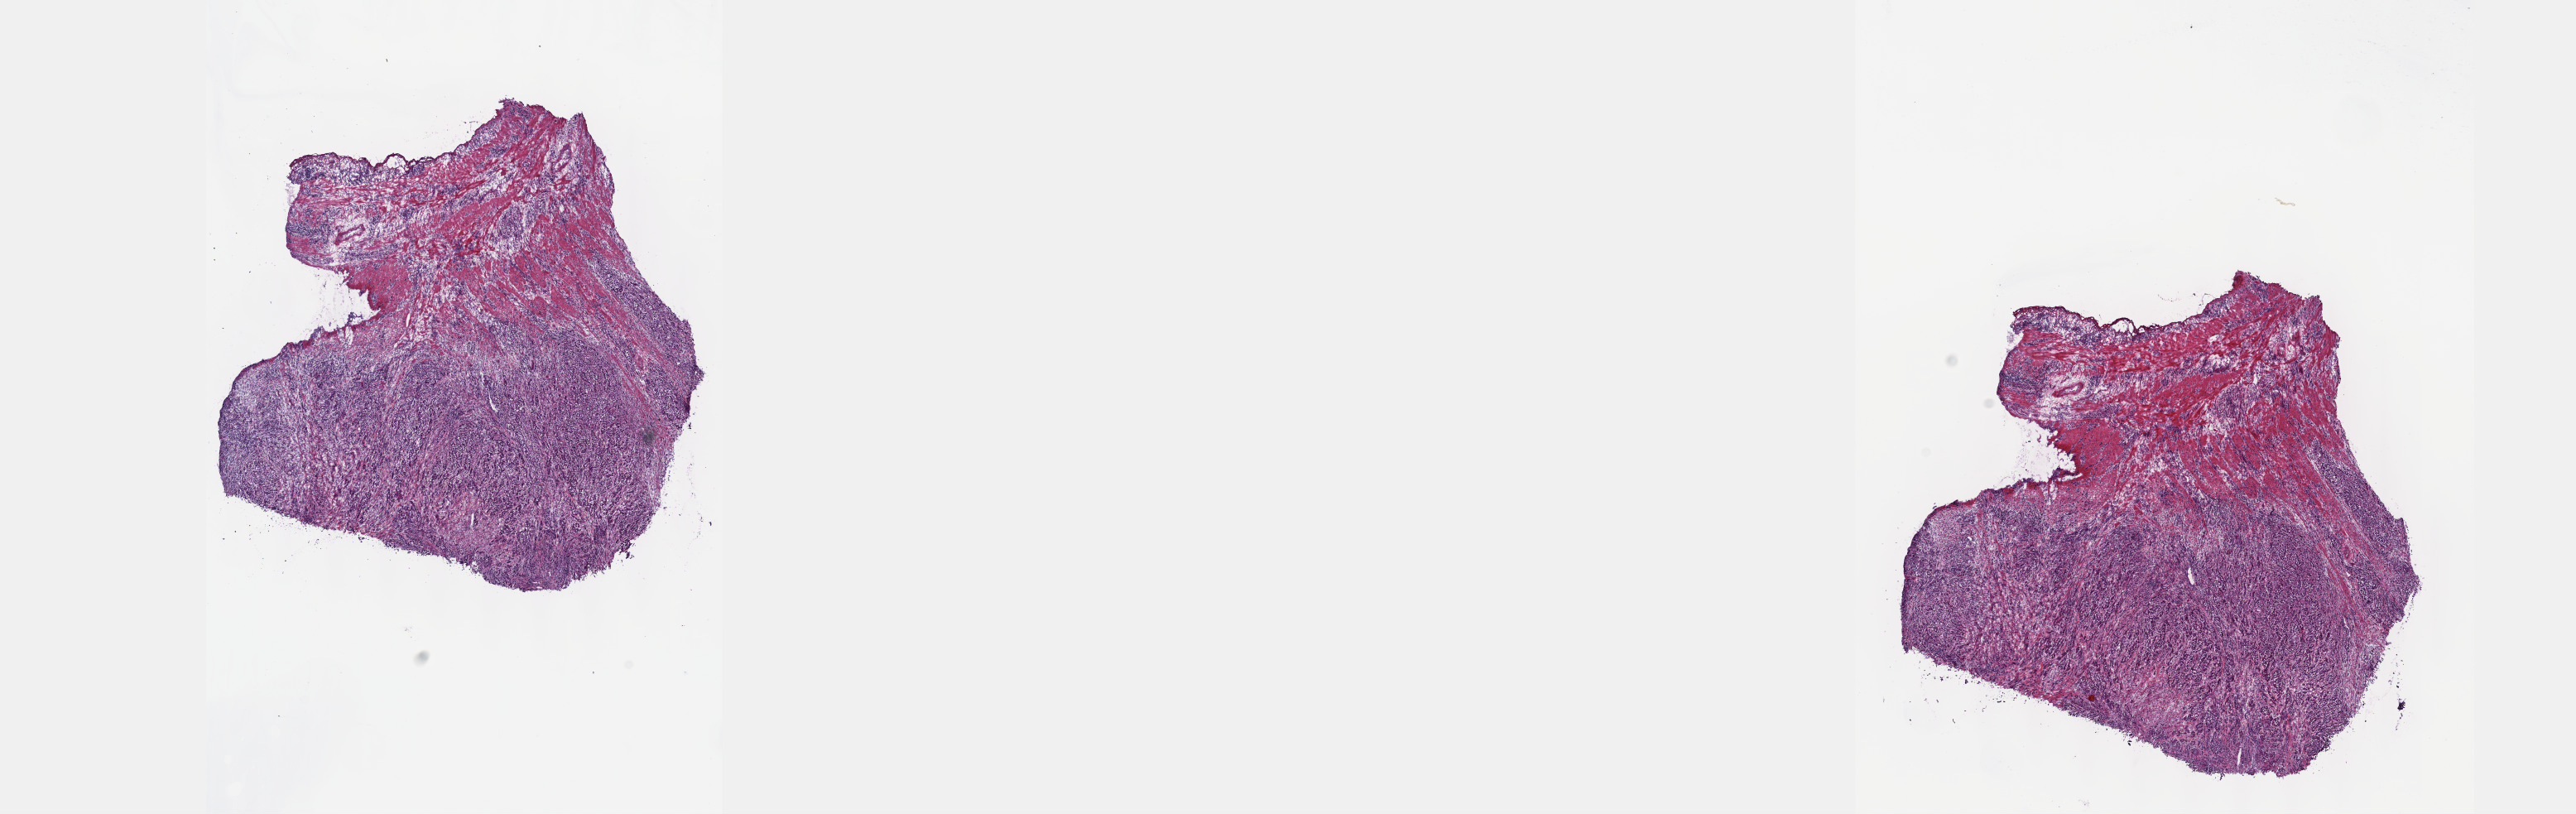
Whole-slide histology image, H&E-stained — low-resolution overview of the scanned area, about 25.1 x 7.9 mm; frozen section; primary tumour sample from the stomach. Male patient; age at initial diagnosis 72 years. Histologic grade: G3 (poorly differentiated). Composition of this section per pathologist review: tumour cells 100%, tumour nuclei 70%, normal cells 0%, stromal cells 0%, necrosis 0%. Infiltration values recorded for this section: lymphocyte infiltration 5%, monocyte infiltration 0%, neutrophil infiltration 0%.
AJCC pathologic stage: IIIB (6th edition). Histologic diagnosis: Adenocarcinoma, intestinal type (gastric antrum). Lymph nodes positive (case pathology): 11 of 12 examined.